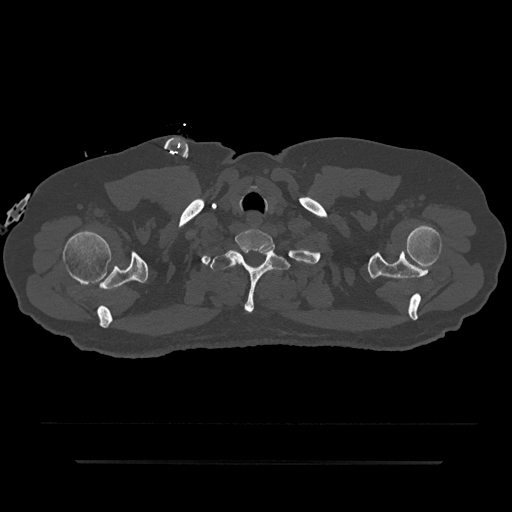
CT including the spine, one axial slice; slice 748 of 797 in the series (ordered by position); bone window (W 1800 / L 400 HU); 0.5 mm slice thickness; 512 × 512 image matrix, field of view 464 × 464 mm. Male patient, age 59 years. From the clinical record (not read from this slice): primary cancer: bile ducts.
Structures marked on this image (semi-automatic segmentation, software-assisted and operator-edited):
- T1 vertebra: bounding box (x1, y1, x2, y2) in pixels: (210, 247, 289, 313)